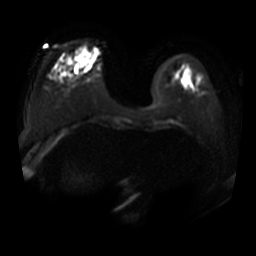
Breast MRI, one axial slice; position 8 of 34 along the scan axis; diffusion-weighted series; image 2 of 4 stored at this slice position (different b-values; order by instance number); 3 T; 5 mm slice thickness; 256 × 256 image matrix, field of view 380 × 380 mm. Female patient.
Outlined on this slice (expert manual segmentation):
- tumour on diffusion-weighted imaging: bounding box [x1, y1, x2, y2] px = [78, 51, 89, 64]